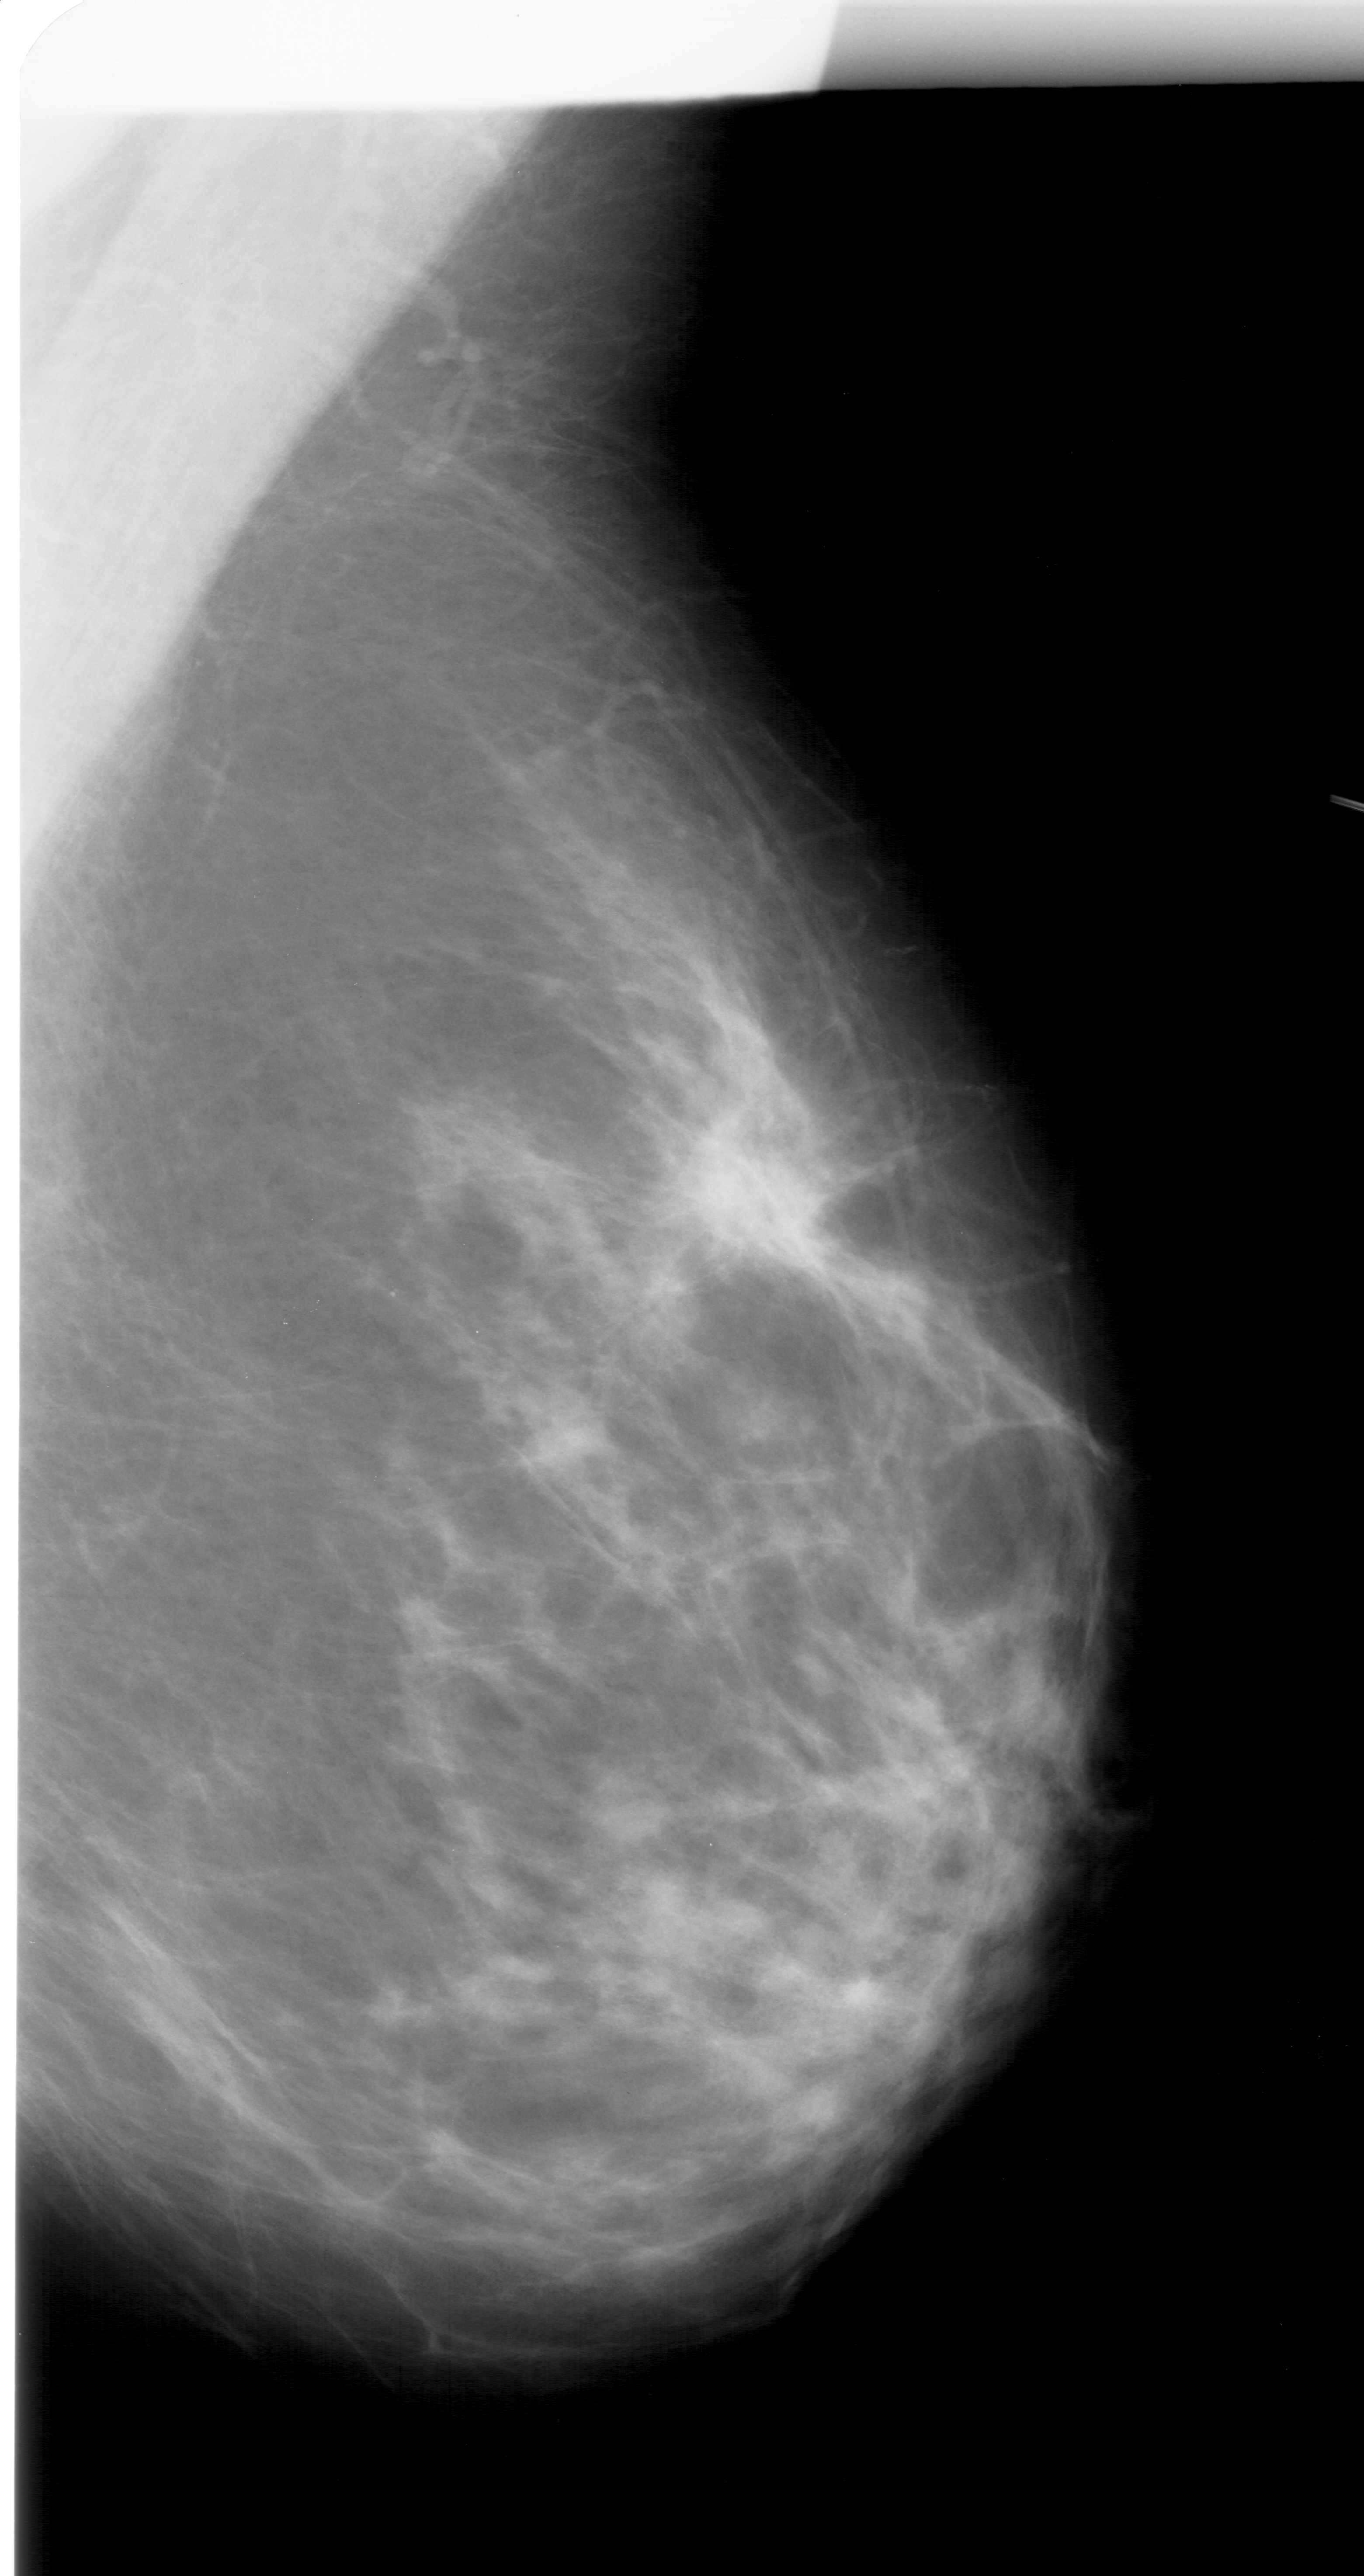
Digitized screen-film mammogram; right breast; mediolateral oblique (MLO) view; breast composition: heterogeneously dense (BI-RADS density category 3 of 4); 1364 × 2576 image matrix.
Marked abnormalities (boxes around the expert regions of interest):
- calcifications, morphology pleomorphic, distribution linear; BI-RADS assessment category 4; pathology (as recorded): benign: box from (x=654, y=1115) to (x=809, y=1237) px